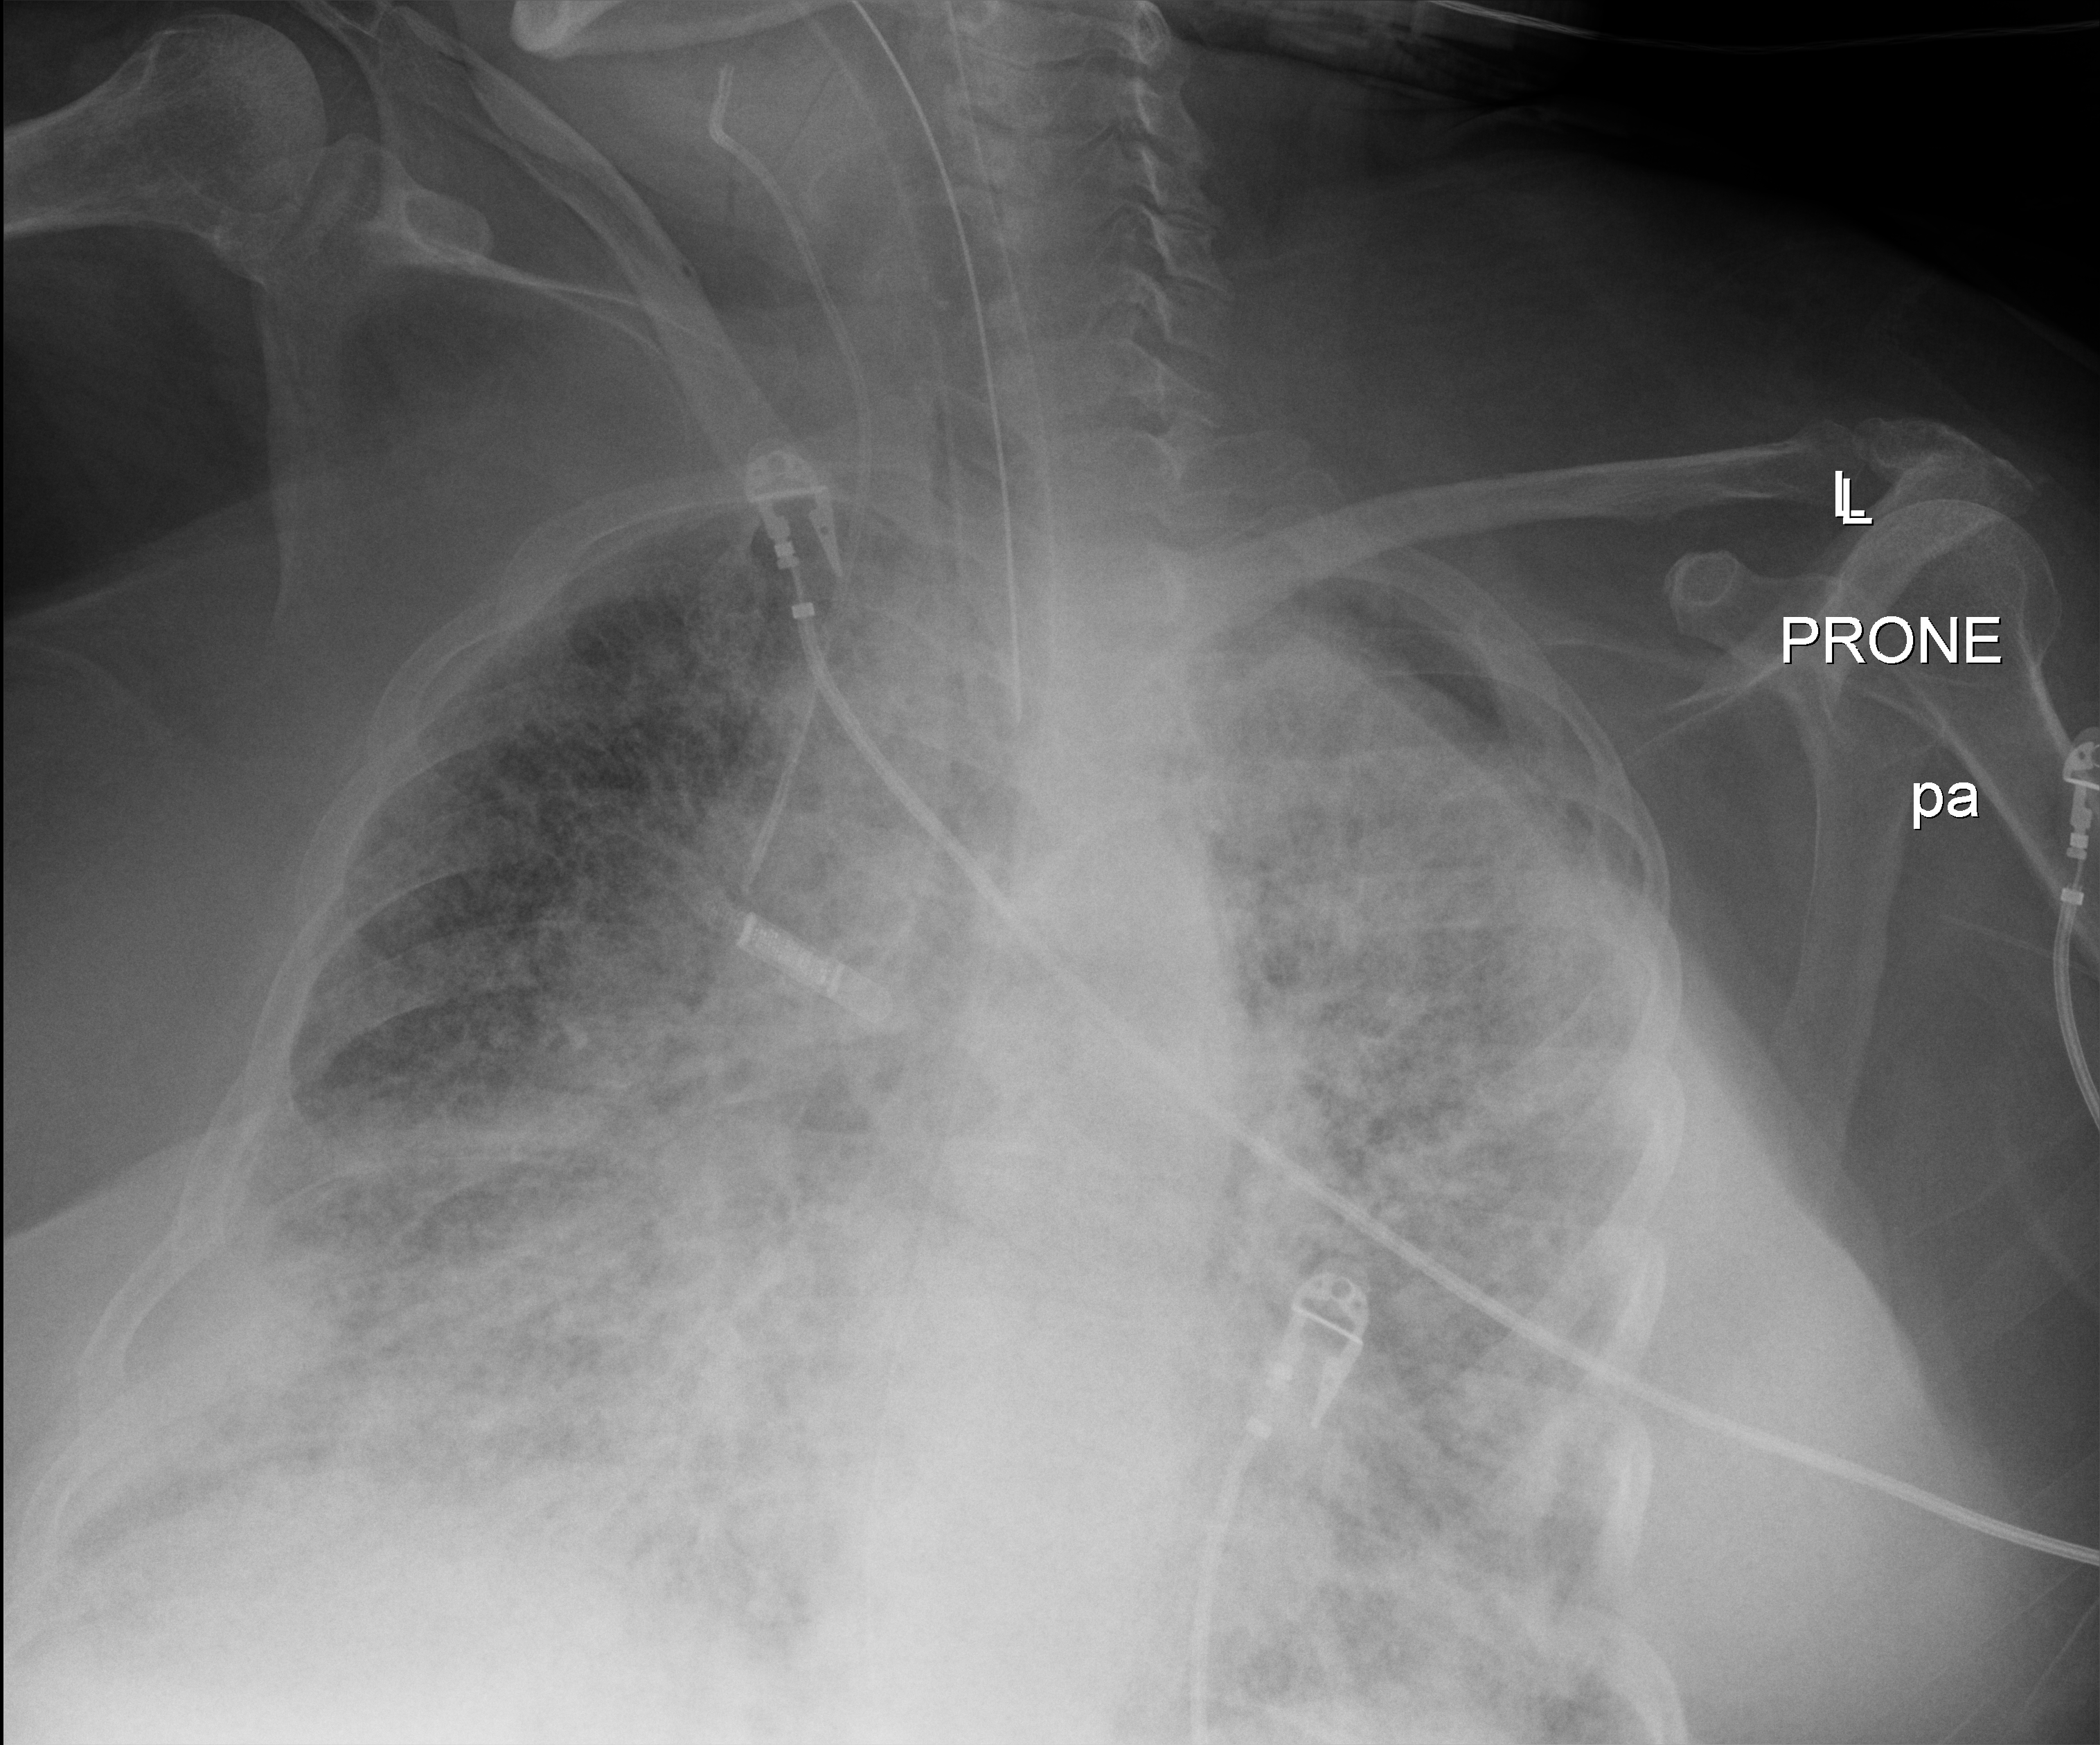
Portable chest radiograph; anteroposterior (AP) projection. Patient hospitalised with COVID-19; female, aged 60–74 years.
Admission-level facts for this patient (not findings on this image; timing relative to this image not recorded): diabetes (admission record): yes; mechanically ventilated during this hospital stay: yes; admitted to intensive care during this hospital stay: yes.